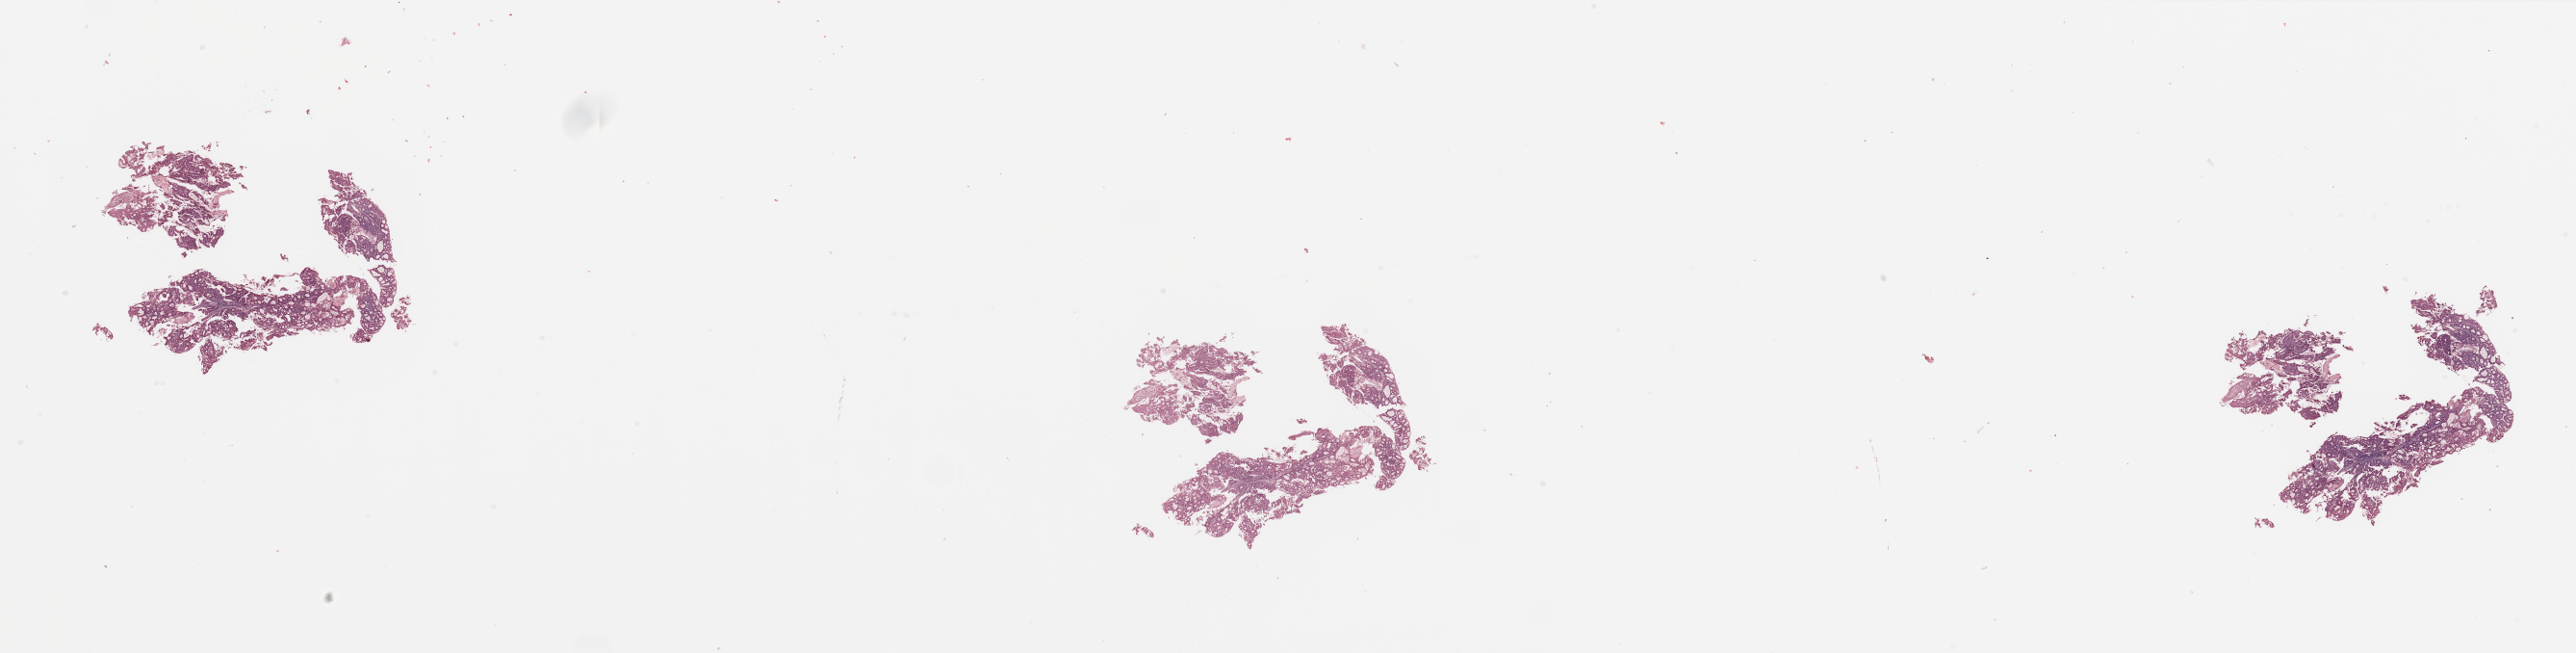
Digitized Hematoxylin and eosin (H&E) stained tissue section (whole slide) — whole scanned area (about 42.3 x 10.7 mm) shown as a low-resolution overview, tumour tissue sample, sampled site: uterus. 80-year-old female patient. Histologic grade: G2 (moderately differentiated). Slide review estimates, as recorded: tumour nuclei 80%, necrosis 2%.
AJCC pathologic stage: I. Primary tumour site (as recorded): anterior endometrium. Diagnosis: Endometrioid adenocarcinoma, NOS.